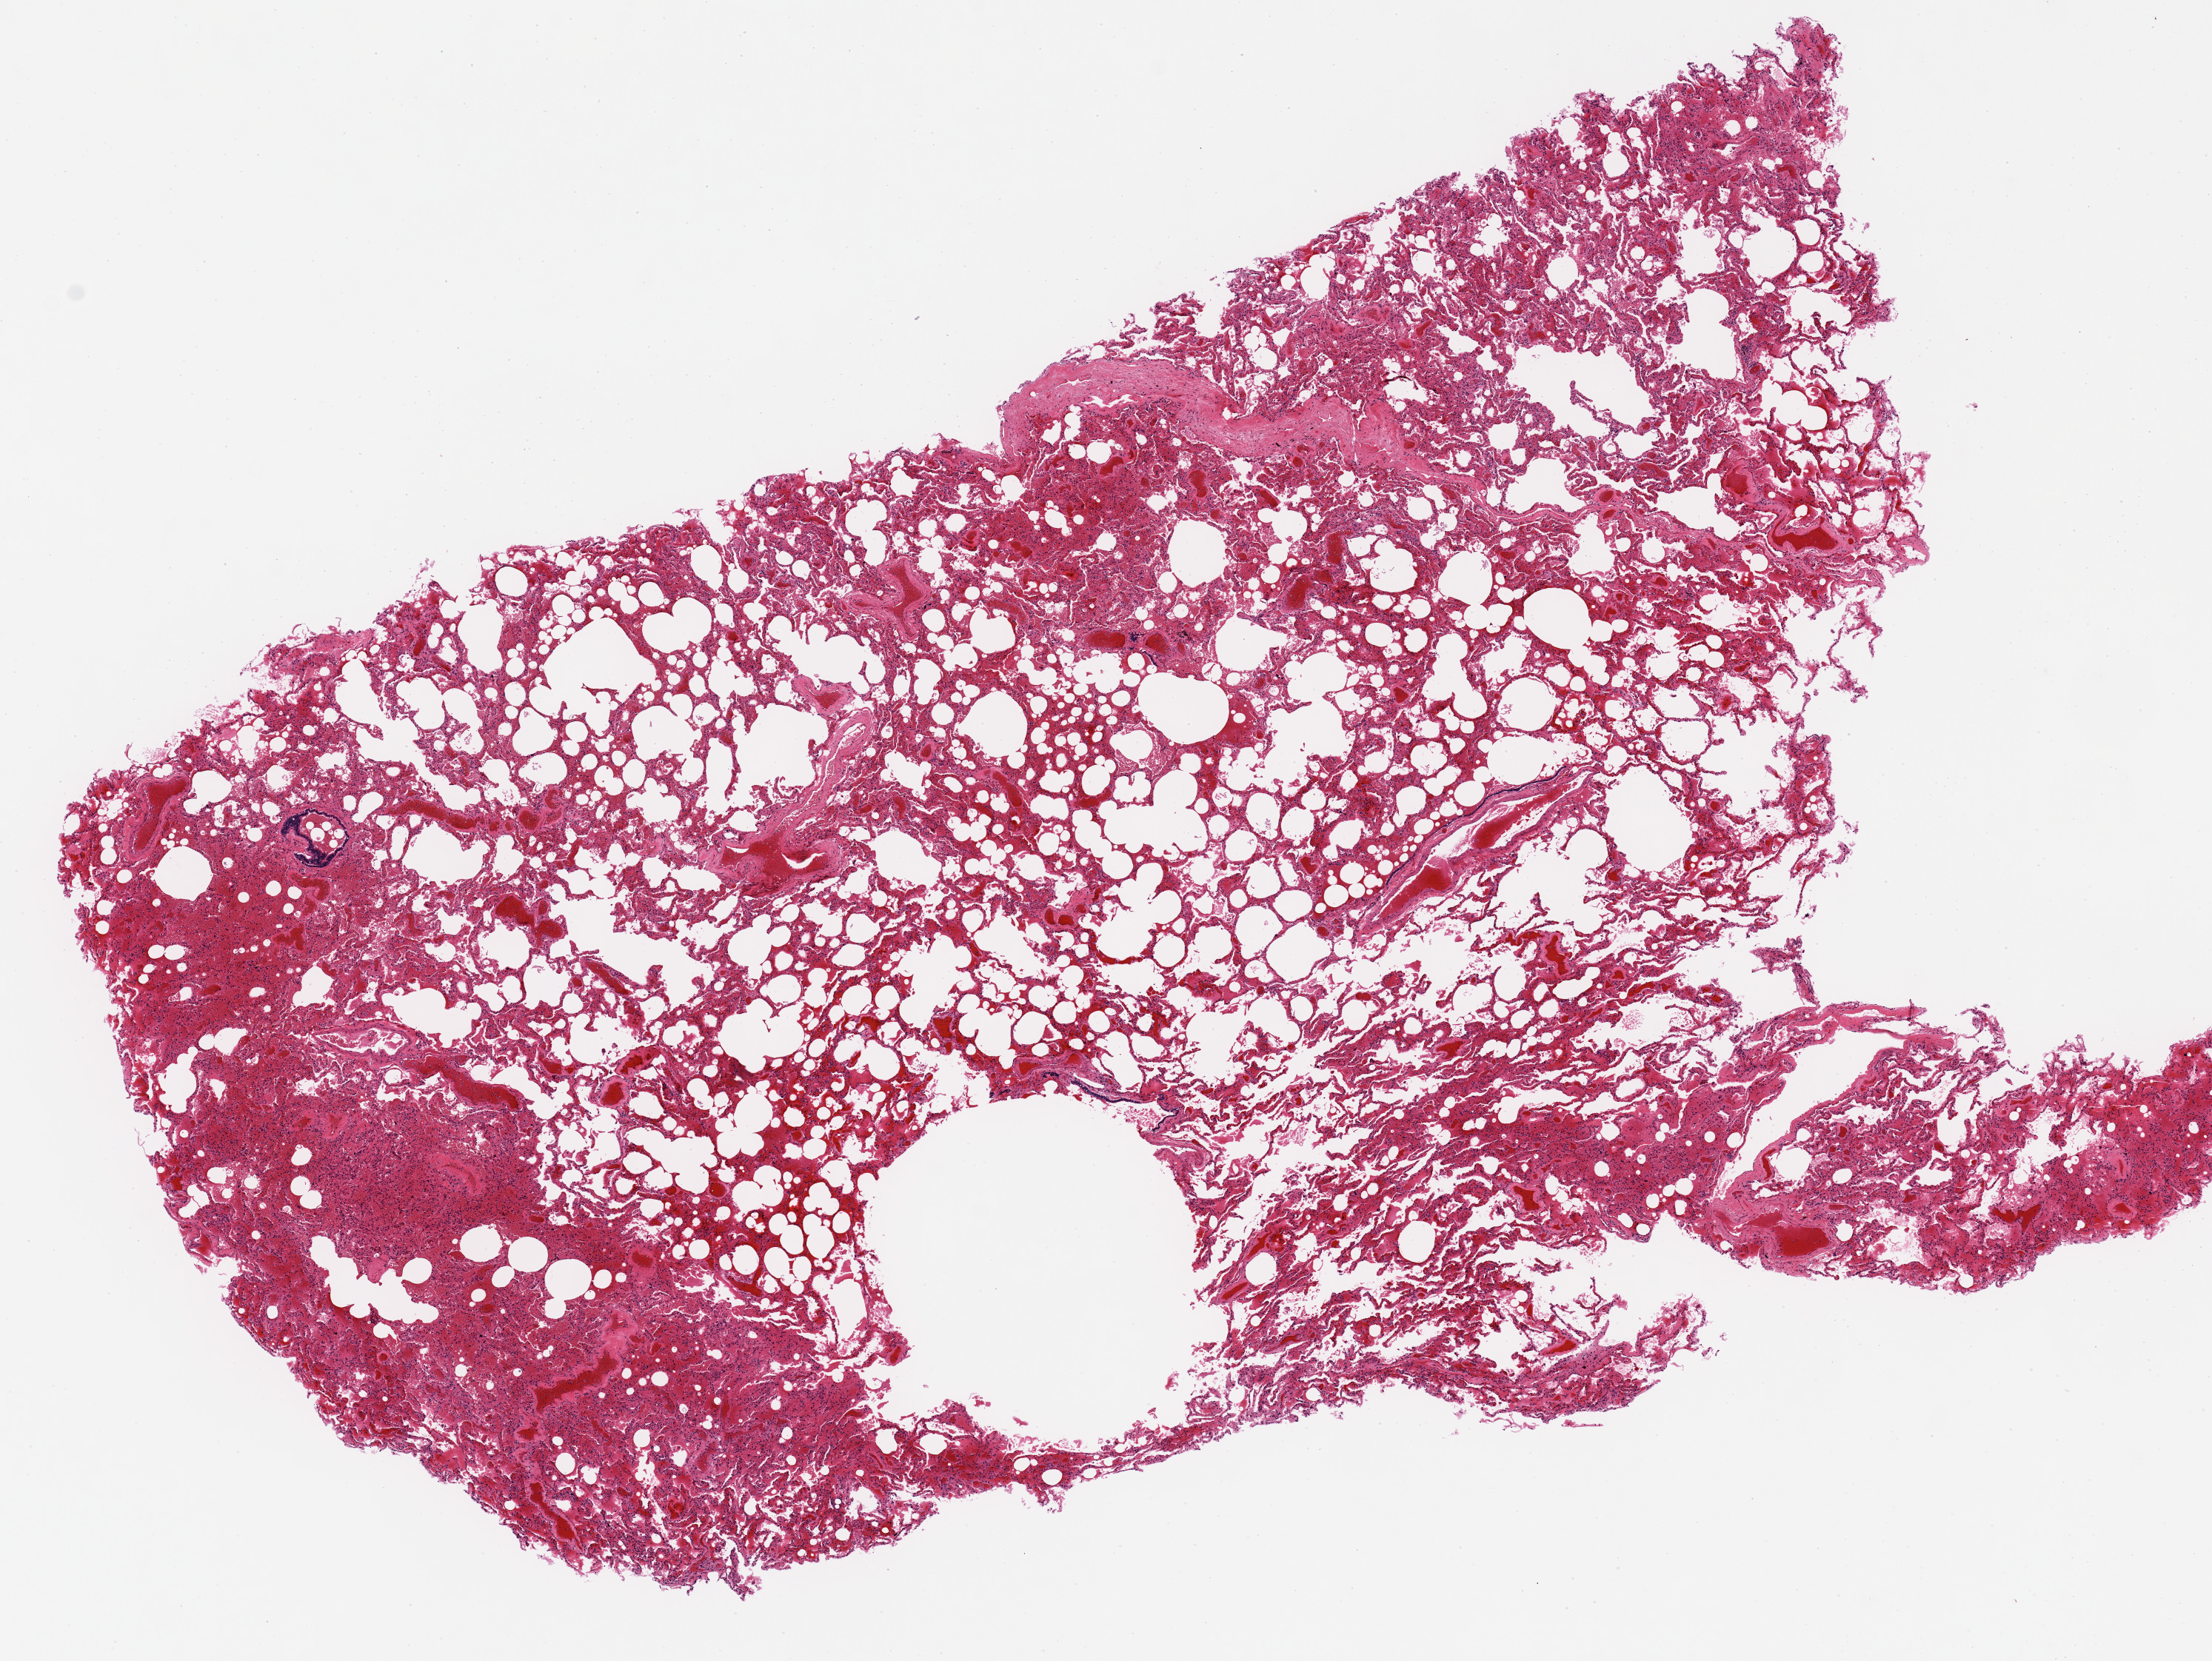
Digitized haematoxylin and eosin-stained section — whole scanned area (about 11.8 x 8.9 mm) shown as a low-resolution overview. PAXgene-fixed, paraffin-embedded tissue. Section of lung (target tissue). Donor tissue sample. Donor sex: male.
- review note (as recorded): moderate congestion; focal hemorrhages